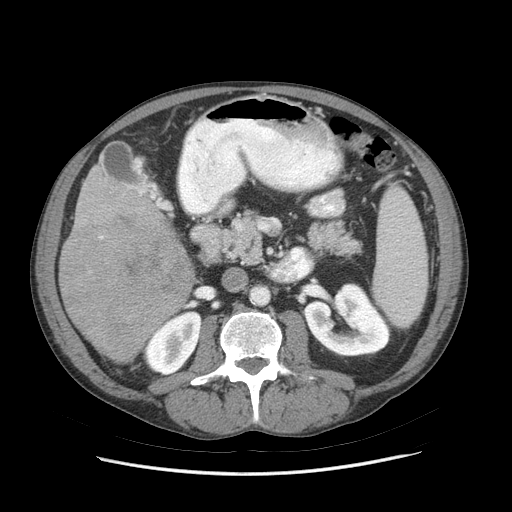
Contrast-enhanced abdominal CT (liver protocol), one axial slice. Position 27 of 89 along the scan axis. Reconstruction kernel STANDARD. 140 kVp. Soft-tissue window (W 400 / L 40 HU). 2.5 mm slice thickness. 512 × 512 image matrix. Case-level facts recorded for this patient, not image findings: diagnosis: hepatocellular carcinoma (patient treated with transarterial chemoembolisation; whether this scan precedes or follows treatment is not stated here); TNM stage (as recorded): Stage-IIIB; Child-Pugh class: A; tumour nodularity: multinodular.
Structures marked on this image (semi-automatically segmented with operator editing):
- liver parenchyma outside the tumour (the mass and vessels are separate outlines, so this box may not span the whole liver): bounding box <58,159,174,362> (left, top, right, bottom; pixels)
- mass: <59,204,193,361>